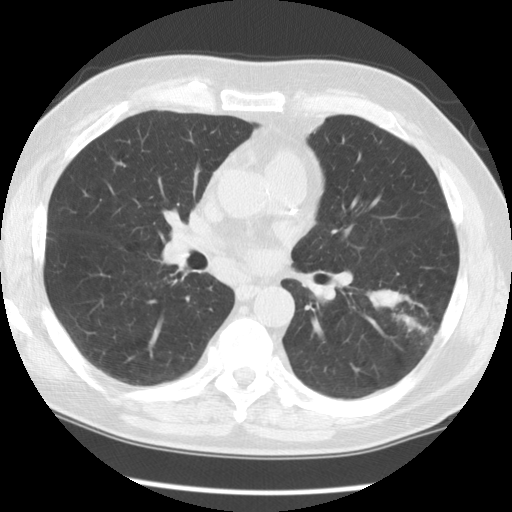
Low-dose screening chest CT, one axial slice; position 72 of 130 along the scan axis; lung window (W 1500 / L -600 HU); 512 × 512 image matrix.
Structures marked on this image (outlined manually by an expert reader):
- lesion 1 (tumor, lower lobe of left lung): bounding box [x1, y1, x2, y2] px = [370, 290, 427, 332]